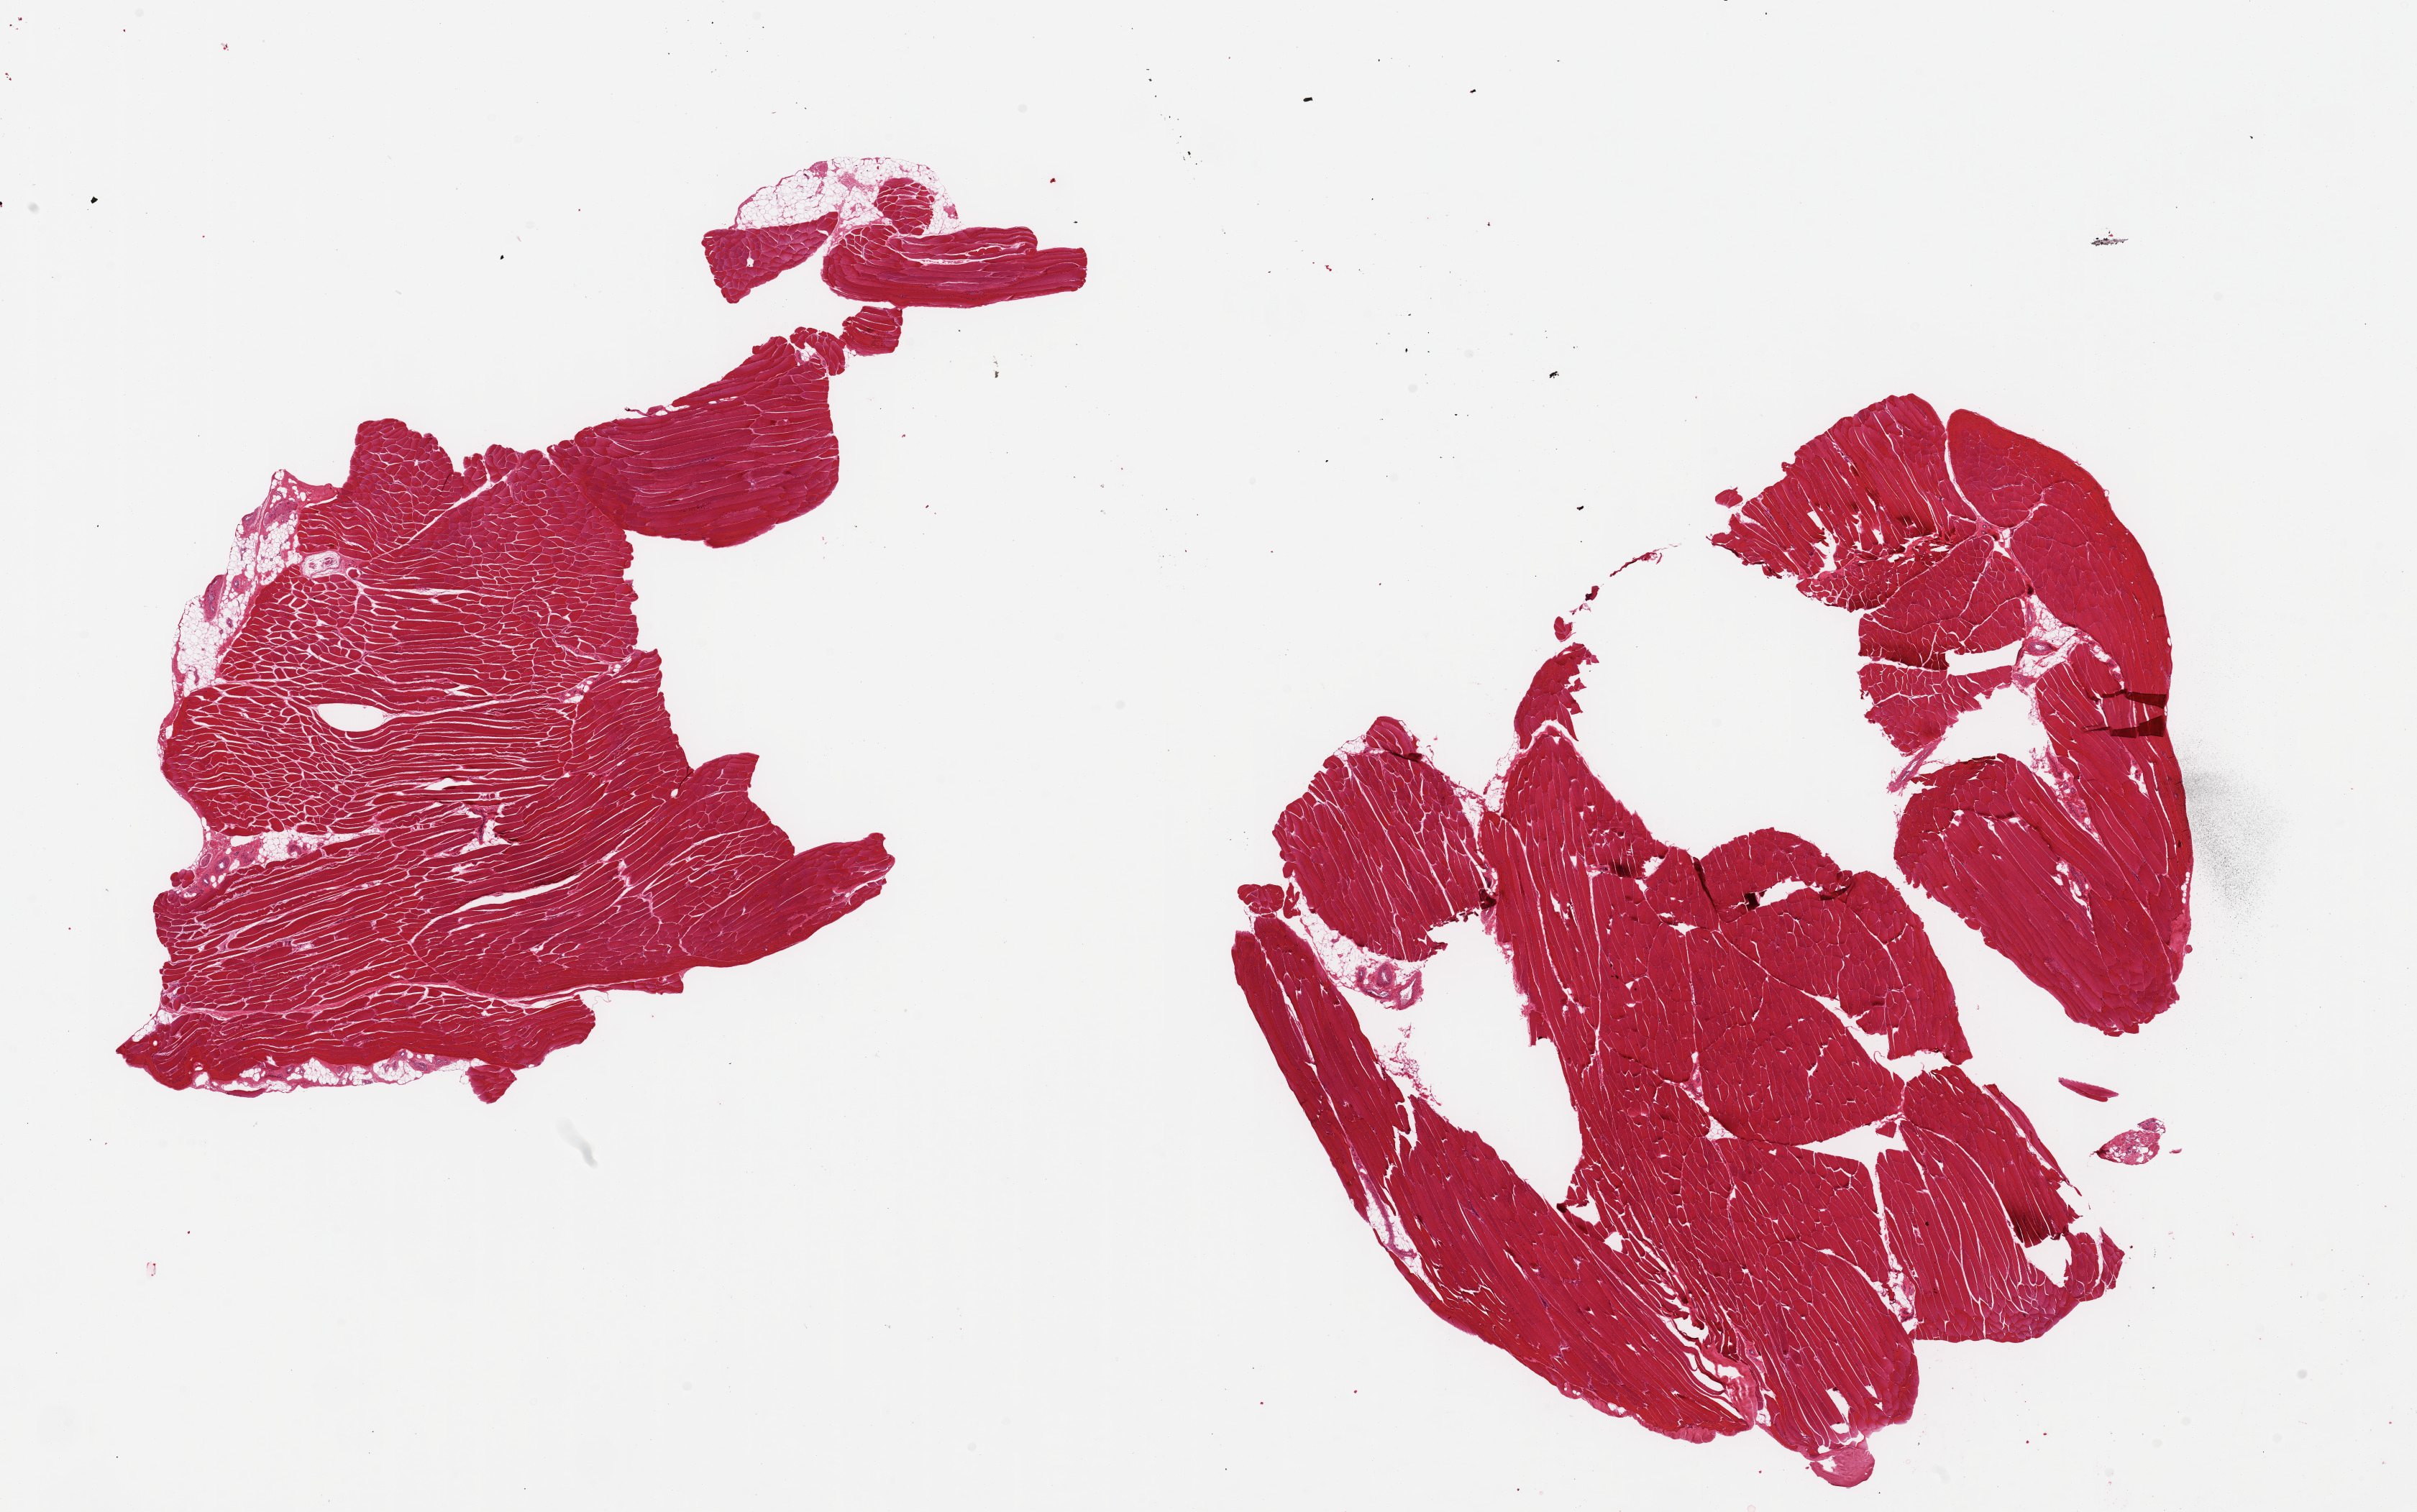
H&E whole-slide image, brightfield, whole scanned area (about 26.6 x 16.6 mm) shown as a low-resolution overview. PAXgene-fixed, paraffin-embedded tissue. Sampled site (target tissue): skeletal muscle. Donor tissue sample. Male donor.
Pathologist's review note for this sample: 2 pieces; incomplete sections, skeletal muscle with ~5% attached fat.